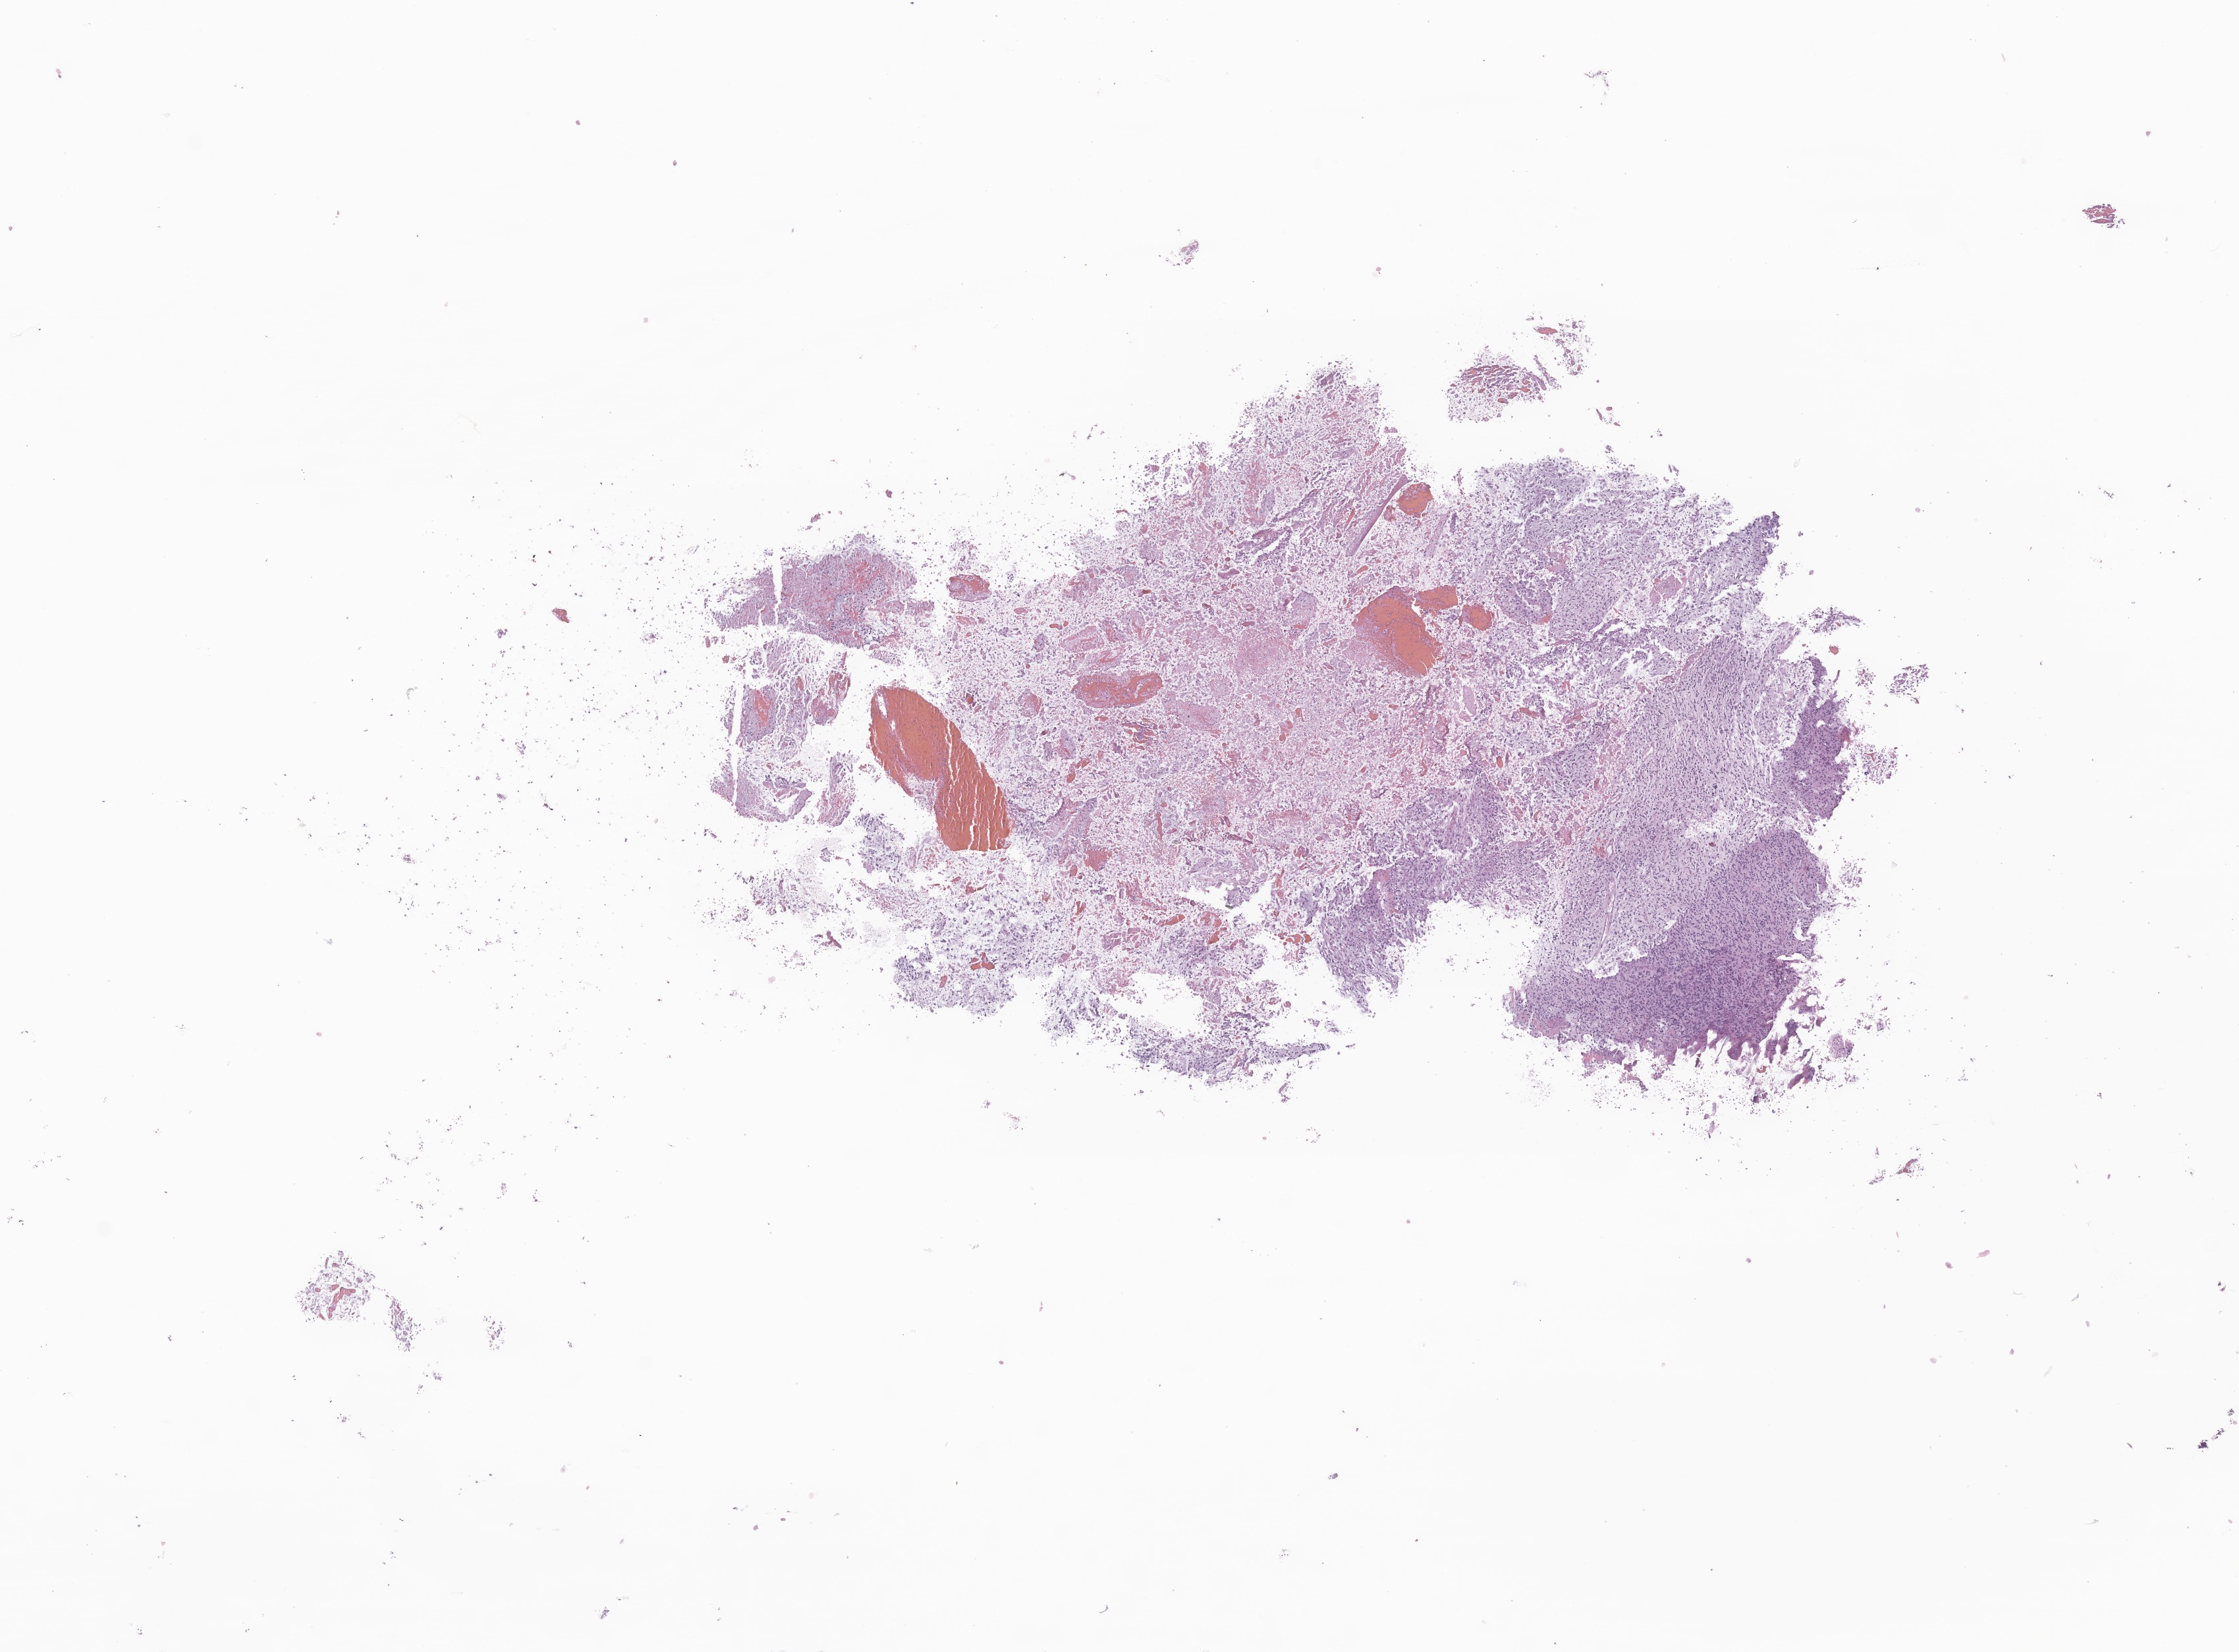
Digitized haematoxylin and eosin-stained section of tumor tissue from the brain stem — a low-resolution overview of the entire scanned area, about 14.3 x 10.6 mm; FFPE section. Male patient, age 180 months (15 years).
• diagnosis: Glioma, malignant